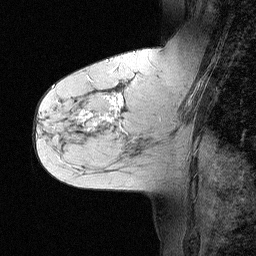
Breast MRI (dynamic contrast-enhanced), one sagittal slice. Position 27 of 64 along the scan axis. Dynamic contrast-enhanced study with each time point stored as its own series, time point 2 of 3 at this slice position (early post-contrast, ordered by acquisition time). 1.5 T. TE 4.5 ms, TR 11 ms. 2.06 mm slice thickness. 256 × 256 image matrix, field of view 200 × 200 mm. Female patient, age 55 years. From the clinical record (not read from this slice): setting: breast cancer imaged before/during neoadjuvant chemotherapy; receptor status: triple-negative.
Outlined on this slice (semi-automatic segmentation, software-assisted and operator-edited):
- analysis volume of interest (the breast-tissue region the enhancement analysis was run in; not a lesion): bounding box <71,63,147,145> (left, top, right, bottom; pixels)
- tumour enhancement mask (voxels above the 90 % enhancement threshold inside the analysis volume of interest): <82,81,126,130>